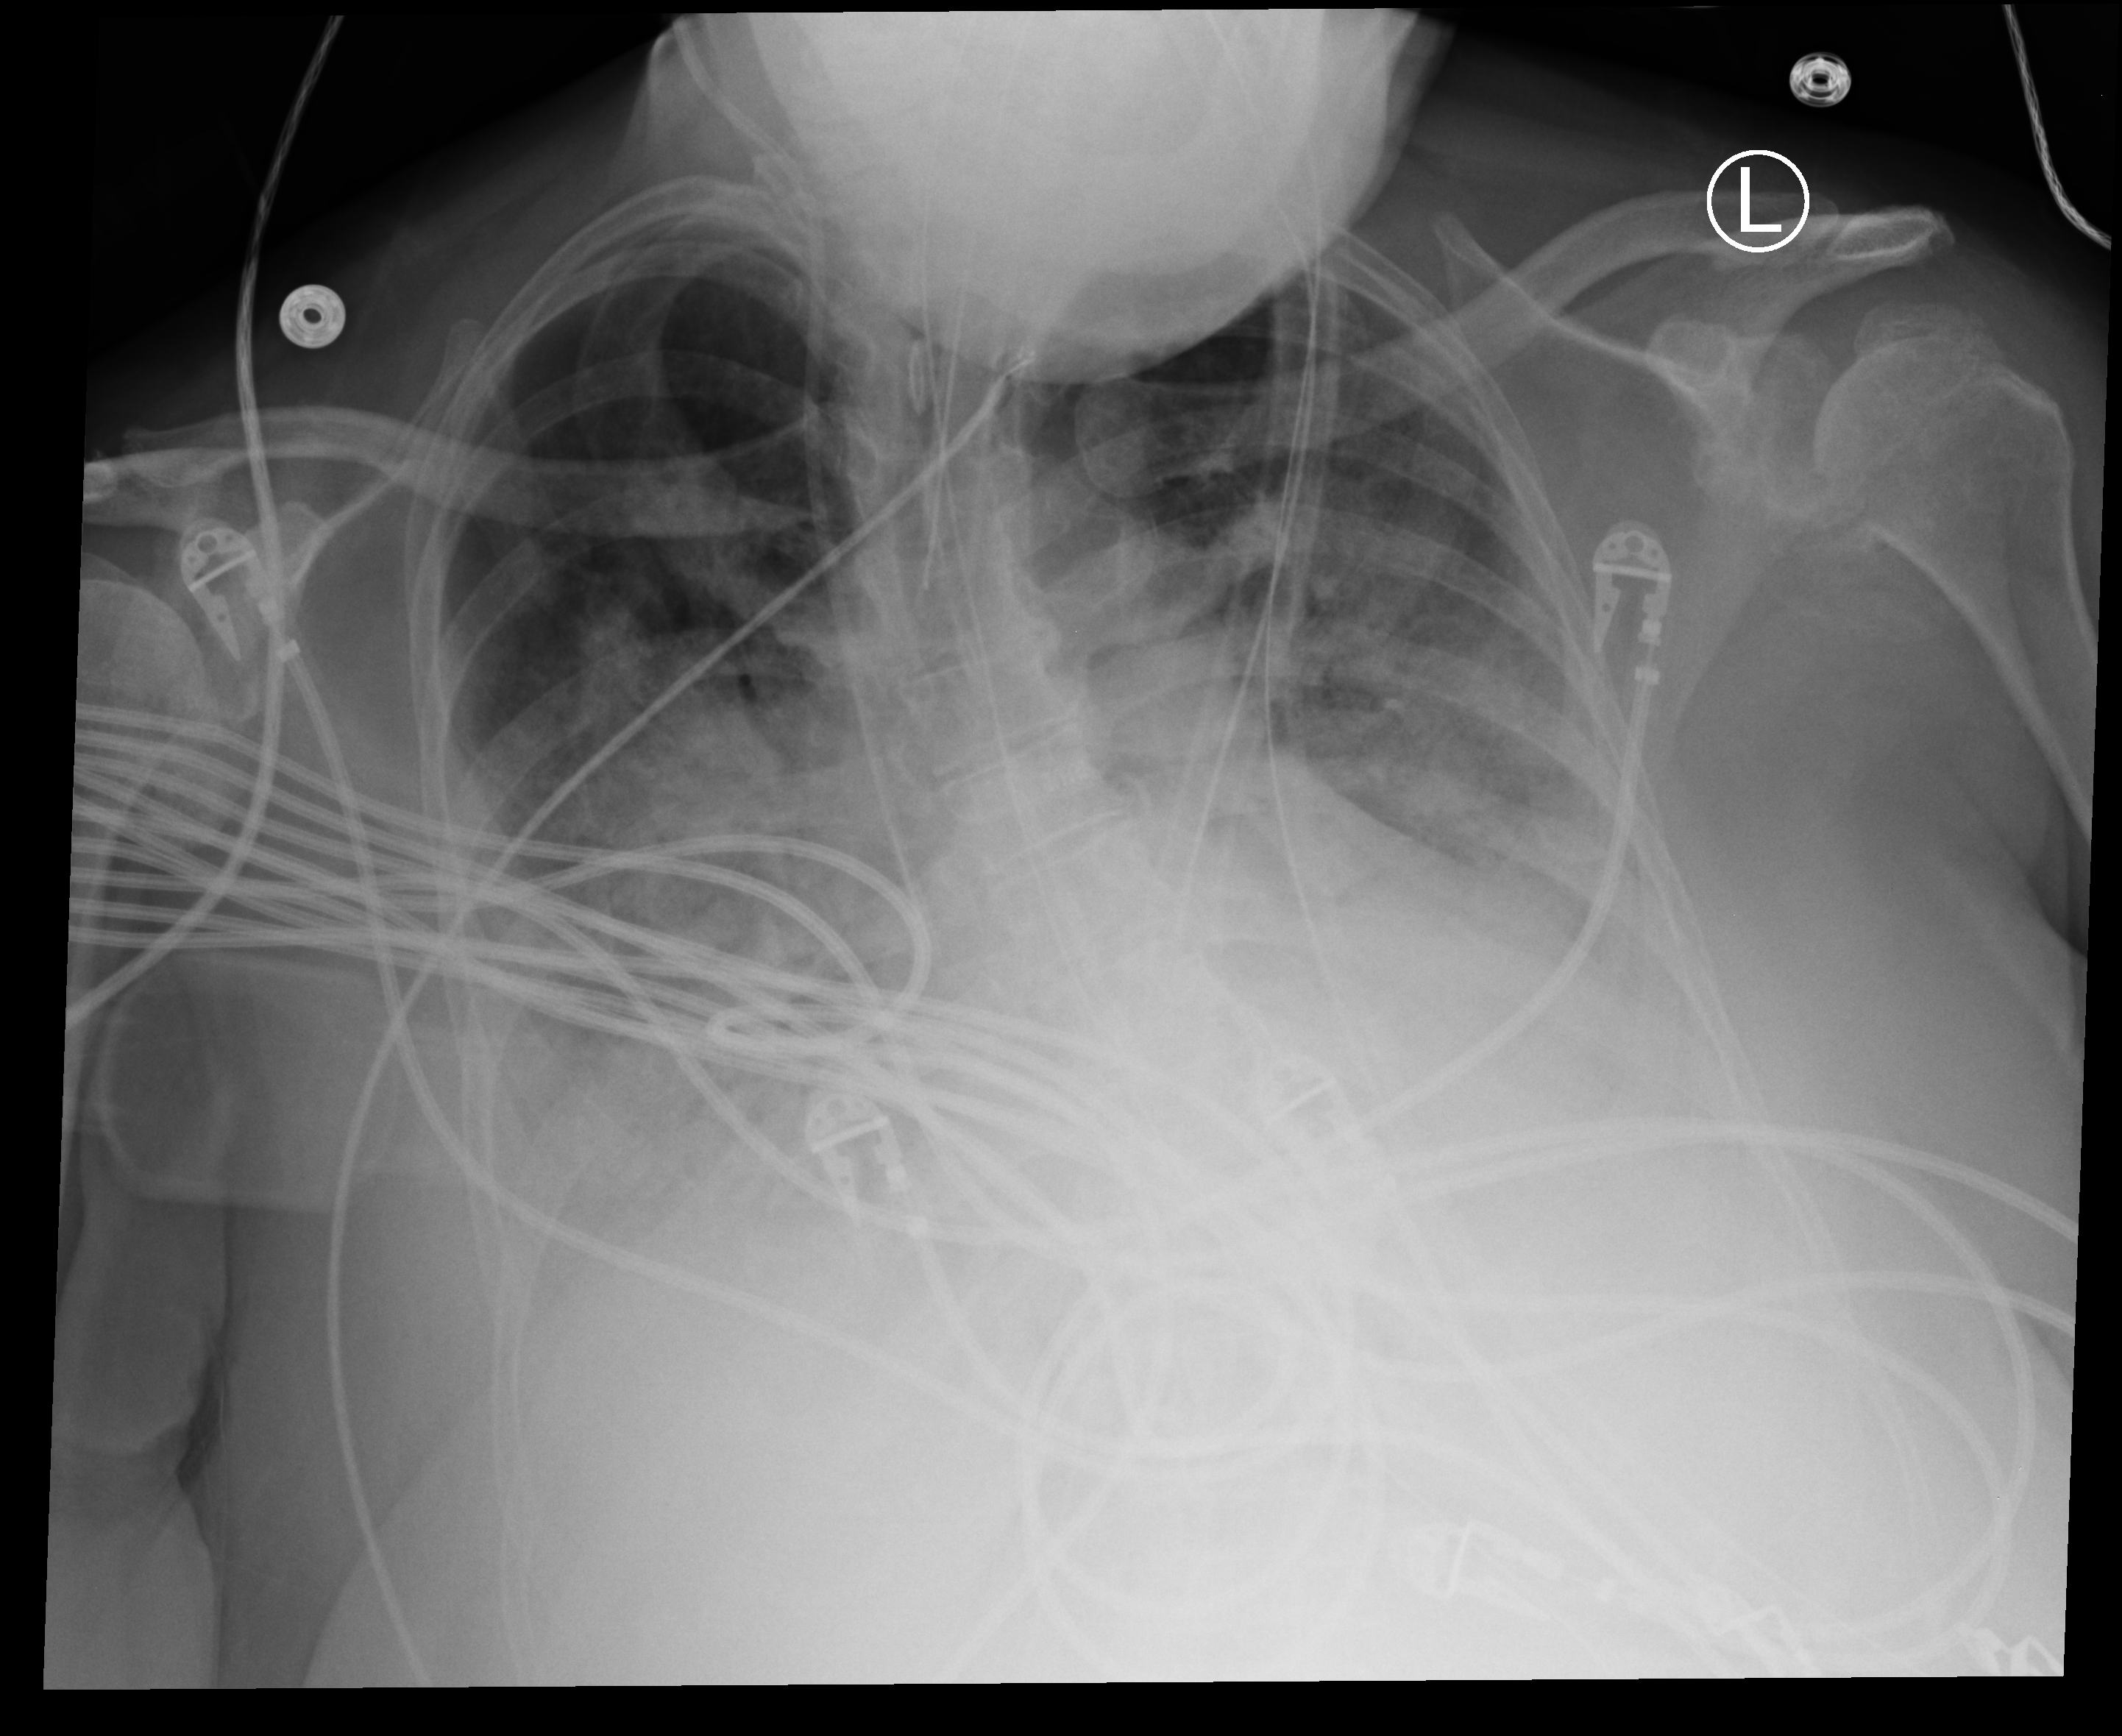
Portable chest radiograph, anteroposterior (AP) projection. Female patient hospitalised with COVID-19, age 60–74 years.
Hospital-stay facts (about this admission, not read from this image; timing relative to this image not recorded):
- mechanically ventilated during this hospital stay: yes